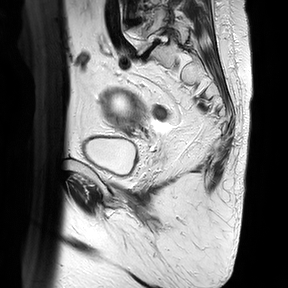
Pelvic MRI for cervical cancer, one sagittal slice. Slice 22 of 30 in the series (ordered by position). T2-weighted. 1.5 T. TE 100 ms, TR 4816.3 ms. 4 mm slice thickness. 288 × 288 image matrix, field of view 300 × 300 mm. Female patient, age 74 years.
Structures marked on this image (manually delineated by an expert):
- uterus and cervix: bounding box <101,86,144,129> (left, top, right, bottom; pixels)